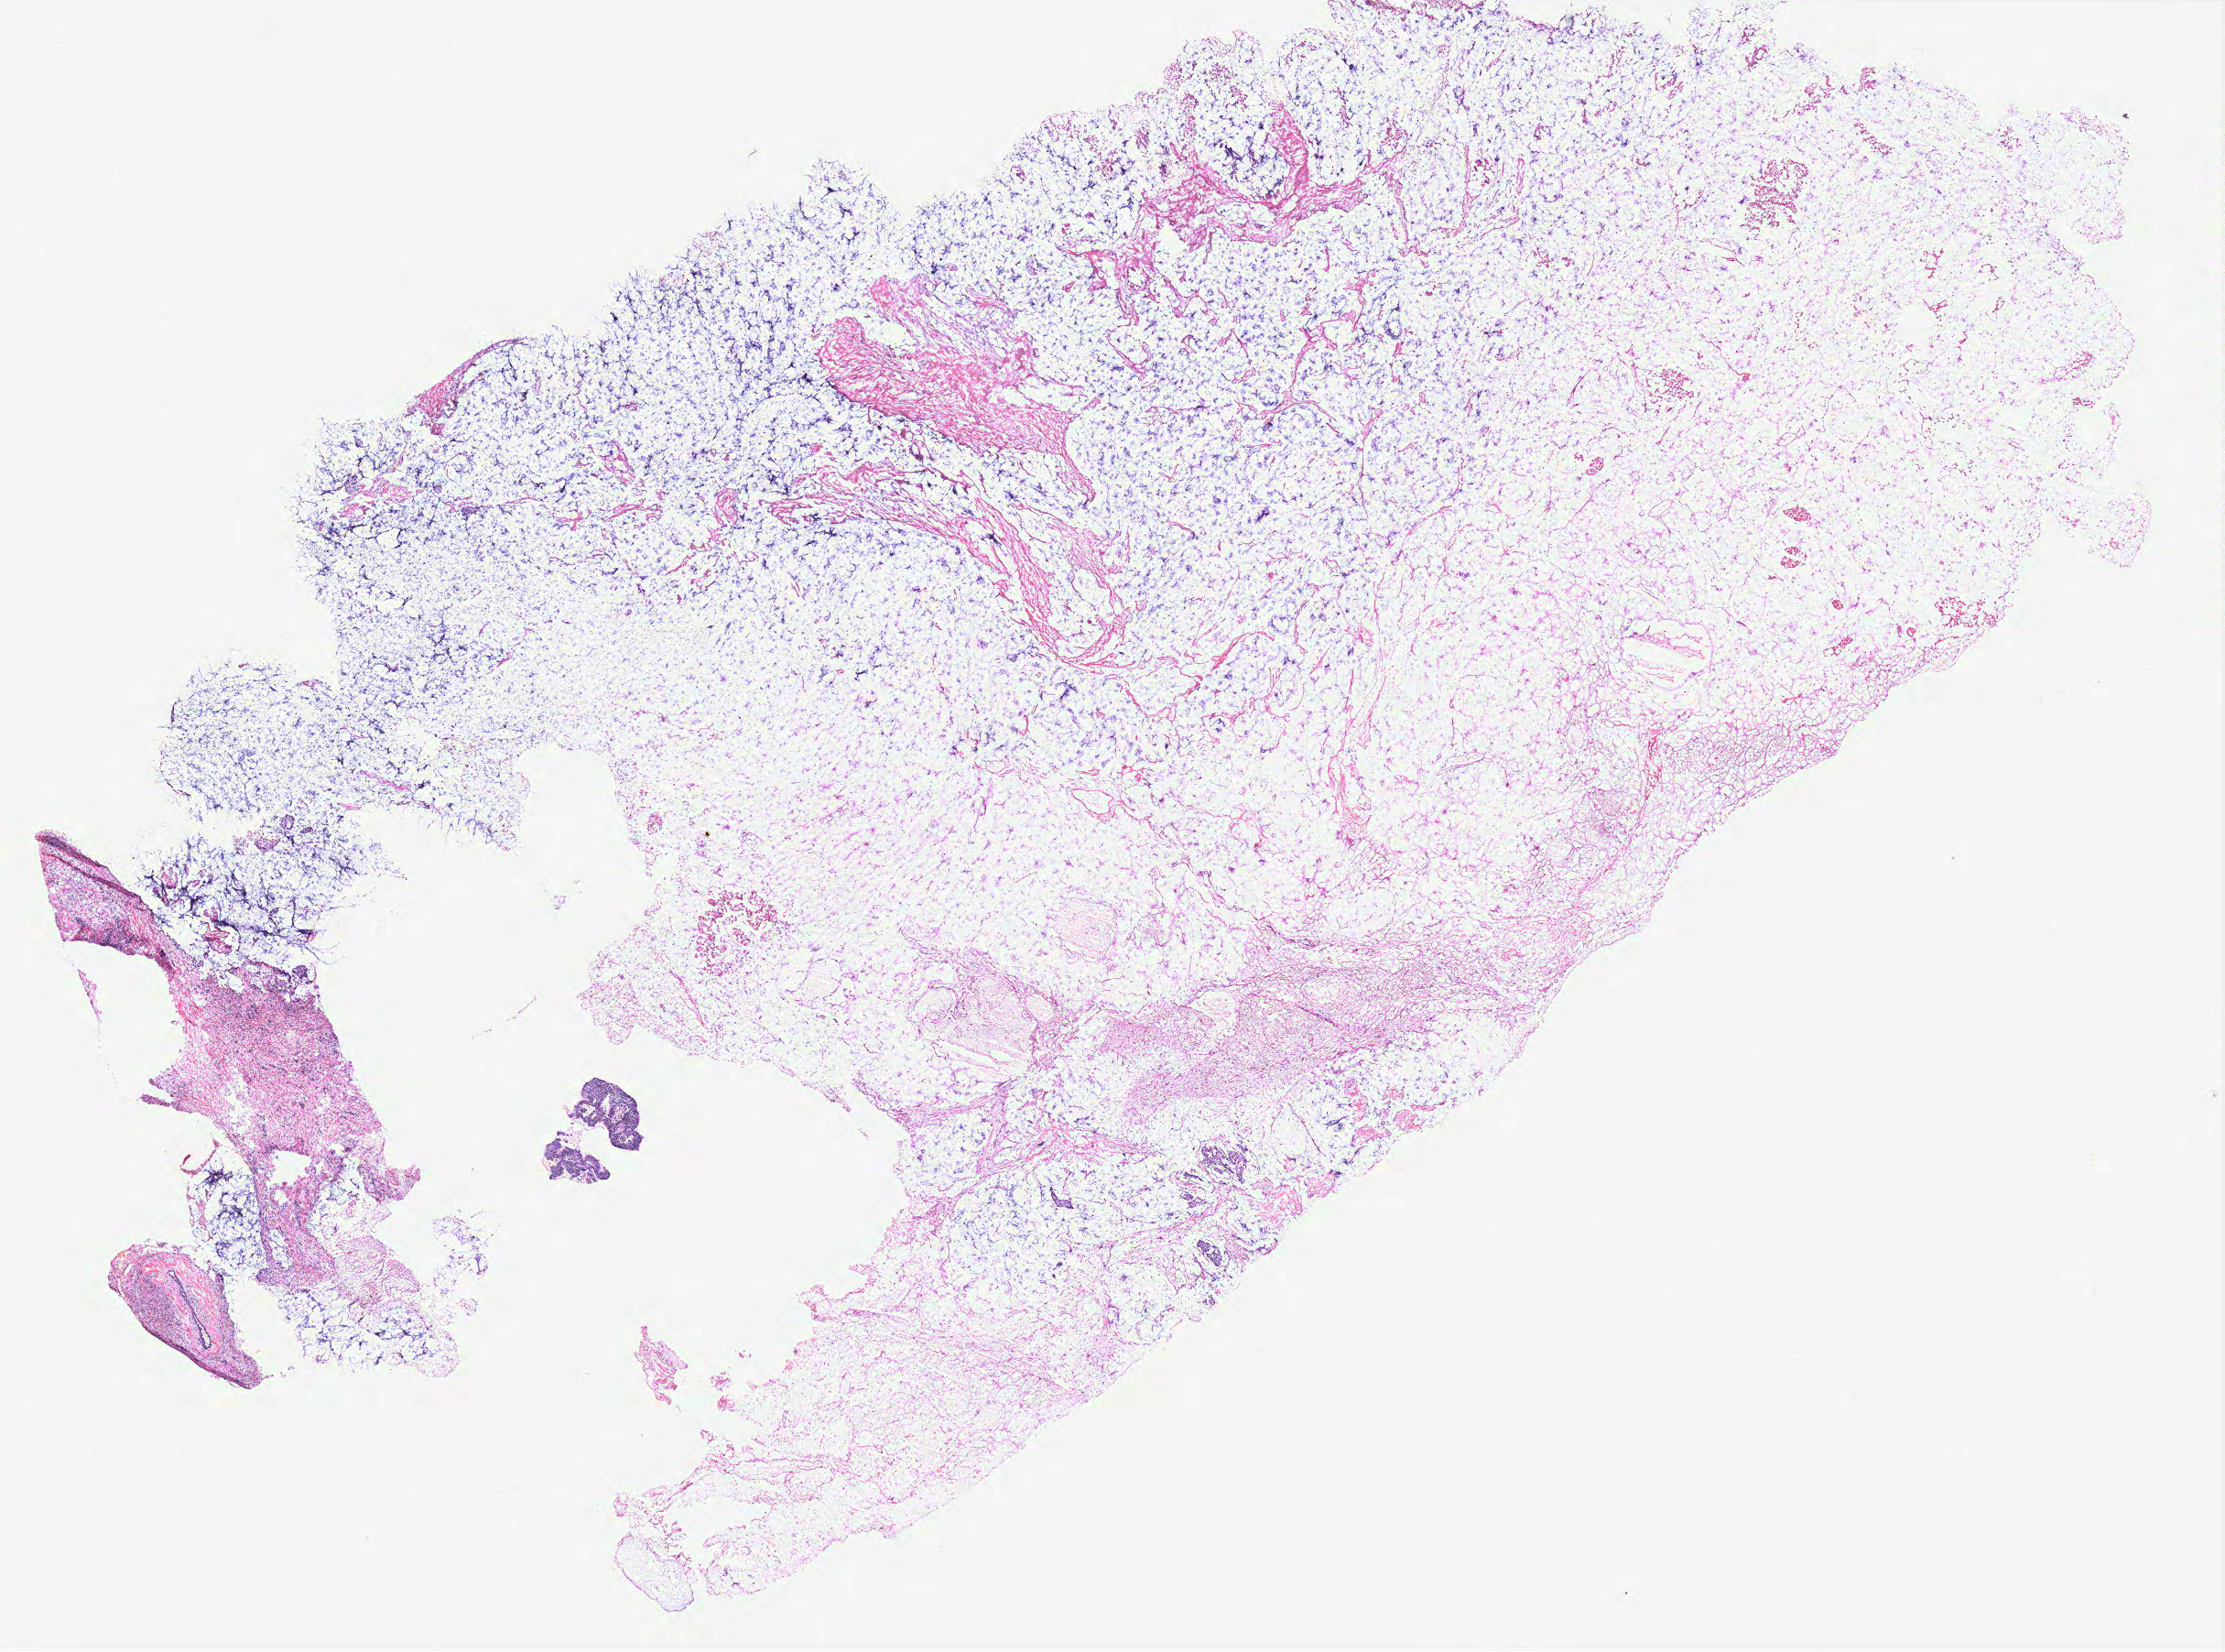
Whole-slide histology image, H&E, low-resolution overview of the scanned area, about 19.4 x 14.4 mm; breast, tissue type not recorded.
Patient diagnosis (cohort enrolment): breast cancer (breast).